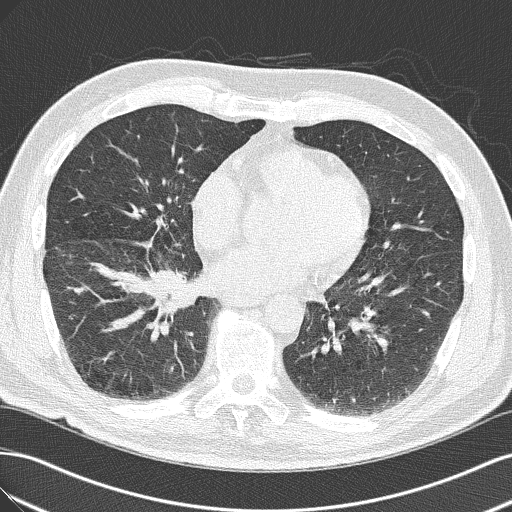
Axial slice from a low-dose chest CT screening exam, baseline screening round, lung window (W 1500 / L -600 HU), 120 kVp. Male, age 65 years at enrolment. Current smoker at enrolment.
- Expert-annotated lung lesion, bounding box (x1, y1, x2, y2) in pixels: (103, 245, 202, 338).
- Screening reader's record for this exam (one nodule recorded; not confirmed to be the boxed lesion): non-calcified nodule or mass ≥4 mm, right upper lobe, 18 × 13 mm, spiculated (stellate) margins, soft tissue attenuation.
- Official screen result: positive, change unspecified: nodule(s) >= 4 mm or enlarging nodule(s), mass(es), or other non-specific abnormalities suspicious for lung cancer.
- Later outcome: lung cancer diagnosed 14 days after this screen — adenocarcinoma, NOS, right lower lobe, poorly differentiated (G3), stage IIIA (AJCC 6th edition), 40 mm at pathology.